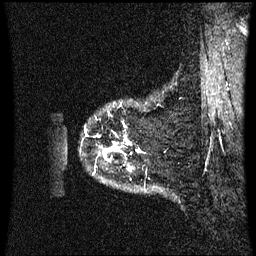
Breast MRI (dynamic contrast-enhanced), one sagittal slice; slice 57 of 60 in the series (ordered by position); dynamic contrast-enhanced series, image 2 of 3 at this slice position (ordered by acquisition); 1.5 T; TE 4.2 ms, TR 8.9 ms; 2.3 mm slice thickness; 256 × 256 image matrix, field of view 210 × 210 mm. Patient: female, 43 years. Case-level facts recorded for this patient, not image findings: setting: breast cancer imaged before/during neoadjuvant chemotherapy; receptor status: HER2-positive.
Annotated regions visible in this slice (semi-automatic segmentation, software-assisted and operator-edited):
- analysis volume of interest (the breast-tissue region the enhancement analysis was run in; not a lesion): bounding box (x1, y1, x2, y2) in pixels: (86, 123, 141, 162)
- tumour enhancement mask (voxels above the 70 % enhancement threshold inside the analysis volume of interest): (99, 136, 141, 153)